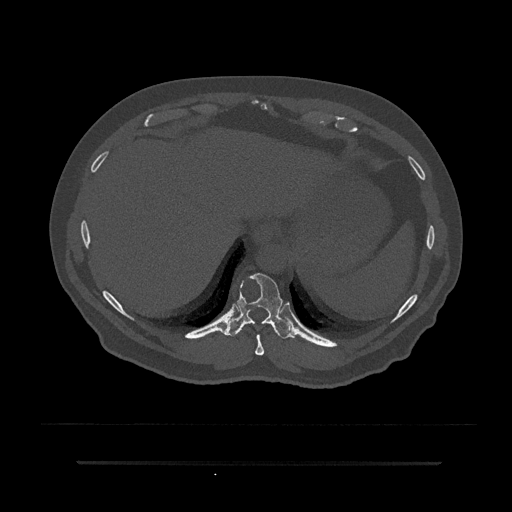
CT including the spine, one axial slice; reconstruction kernel Br40s/3; 120 kVp; bone window (W 1800 / L 400 HU); 512 × 512 image matrix, field of view 464 × 464 mm. Male patient, age 59 years. From the clinical record (not read from this slice): primary cancer: bile ducts.
Annotated regions visible in this slice (semi-automatically segmented with operator editing):
- T10 vertebra: bounding box [x1, y1, x2, y2] px = [225, 273, 294, 339]
- T9 vertebra: [255, 334, 264, 356]